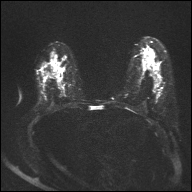
Breast MRI, one axial slice. Slice 19 of 32 in the series (ordered by position). Diffusion-weighted series; image 2 of 4 stored at this slice position (different b-values; order by instance number). 1.5 T. 4 mm slice thickness. 192 × 192 image matrix, field of view 360 × 360 mm. Female patient.
Annotated regions visible in this slice (outlined manually by an expert reader):
- tumour on diffusion-weighted imaging: bounding box <155,86,161,91> (left, top, right, bottom; pixels)